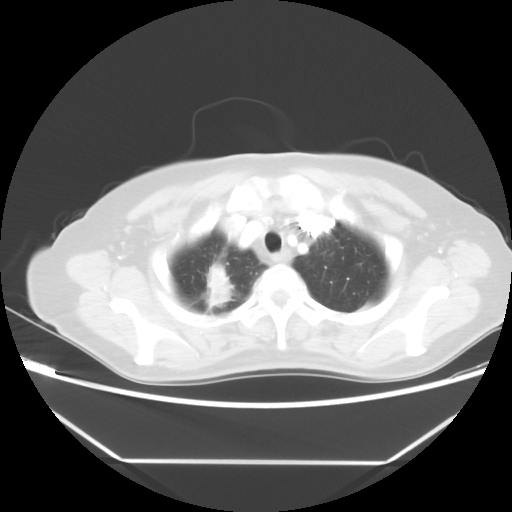
Chest CT, one axial slice. Position 43 of 48 along the scan axis. 100 kVp. Lung window (W 1500 / L -600 HU). 512 × 512 image matrix. Female patient, age 65 years. From the clinical record (not read from this slice): clinical TNM (as recorded): T1c N1 M1.
Structures marked on this image (rectangle marked by the reading radiologist):
- lung tumour (recorded histology: adenocarcinoma): bounding box [x1, y1, x2, y2] px = [206, 262, 234, 314]